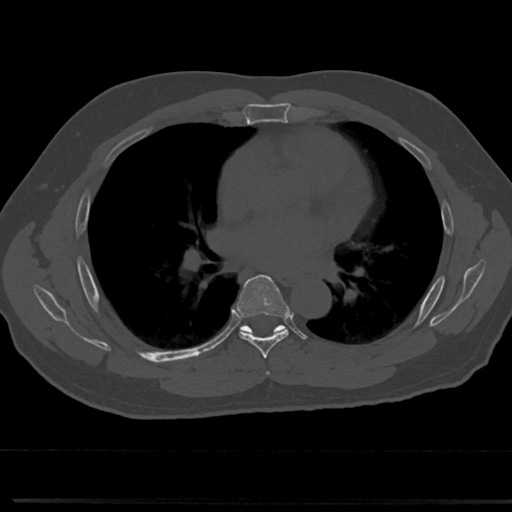
CT including the spine, one axial slice. Slice 440 of 817 in the series (ordered by position). Bone window (W 1800 / L 400 HU). 512 × 512 image matrix, field of view 355 × 355 mm. Male patient, age 61 years. Case-level facts recorded for this patient, not image findings: primary cancer: prostate.
Annotated regions visible in this slice (semi-automatic segmentation, software-assisted and operator-edited):
- T5 vertebra: bounding box [x1, y1, x2, y2] px = [264, 359, 273, 377]
- T6 vertebra: [222, 277, 309, 352]